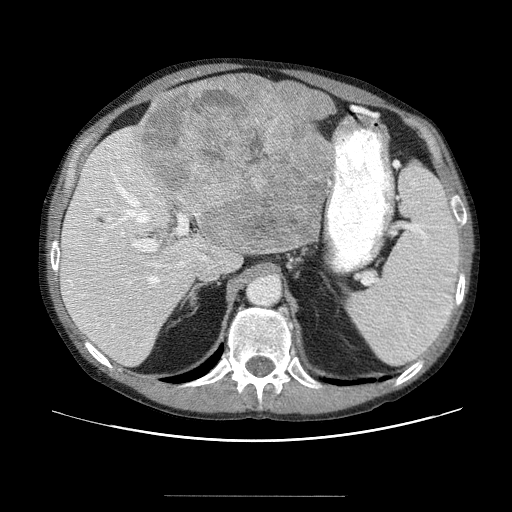
Contrast-enhanced abdominal CT (liver protocol), one axial slice. Position 32 of 69 along the scan axis. Reconstruction kernel STANDARD. 120 kVp. Soft-tissue window (W 400 / L 40 HU). 2.5 mm slice thickness. 512 × 512 image matrix, field of view 380 × 380 mm. Case-level facts recorded for this patient, not image findings: diagnosis: hepatocellular carcinoma (patient treated with transarterial chemoembolisation; whether this scan precedes or follows treatment is not stated here); TNM stage (as recorded): Stage-IVB; Child-Pugh class: B; tumour nodularity: multinodular.
Outlined on this slice (semi-automatic segmentation, software-assisted and operator-edited):
- liver parenchyma outside the tumour (the mass and vessels are separate outlines, so this box may not span the whole liver): bounding box [x1, y1, x2, y2] px = [60, 88, 332, 364]
- mass: [134, 74, 335, 256]
- liver vessels: [70, 149, 222, 348]